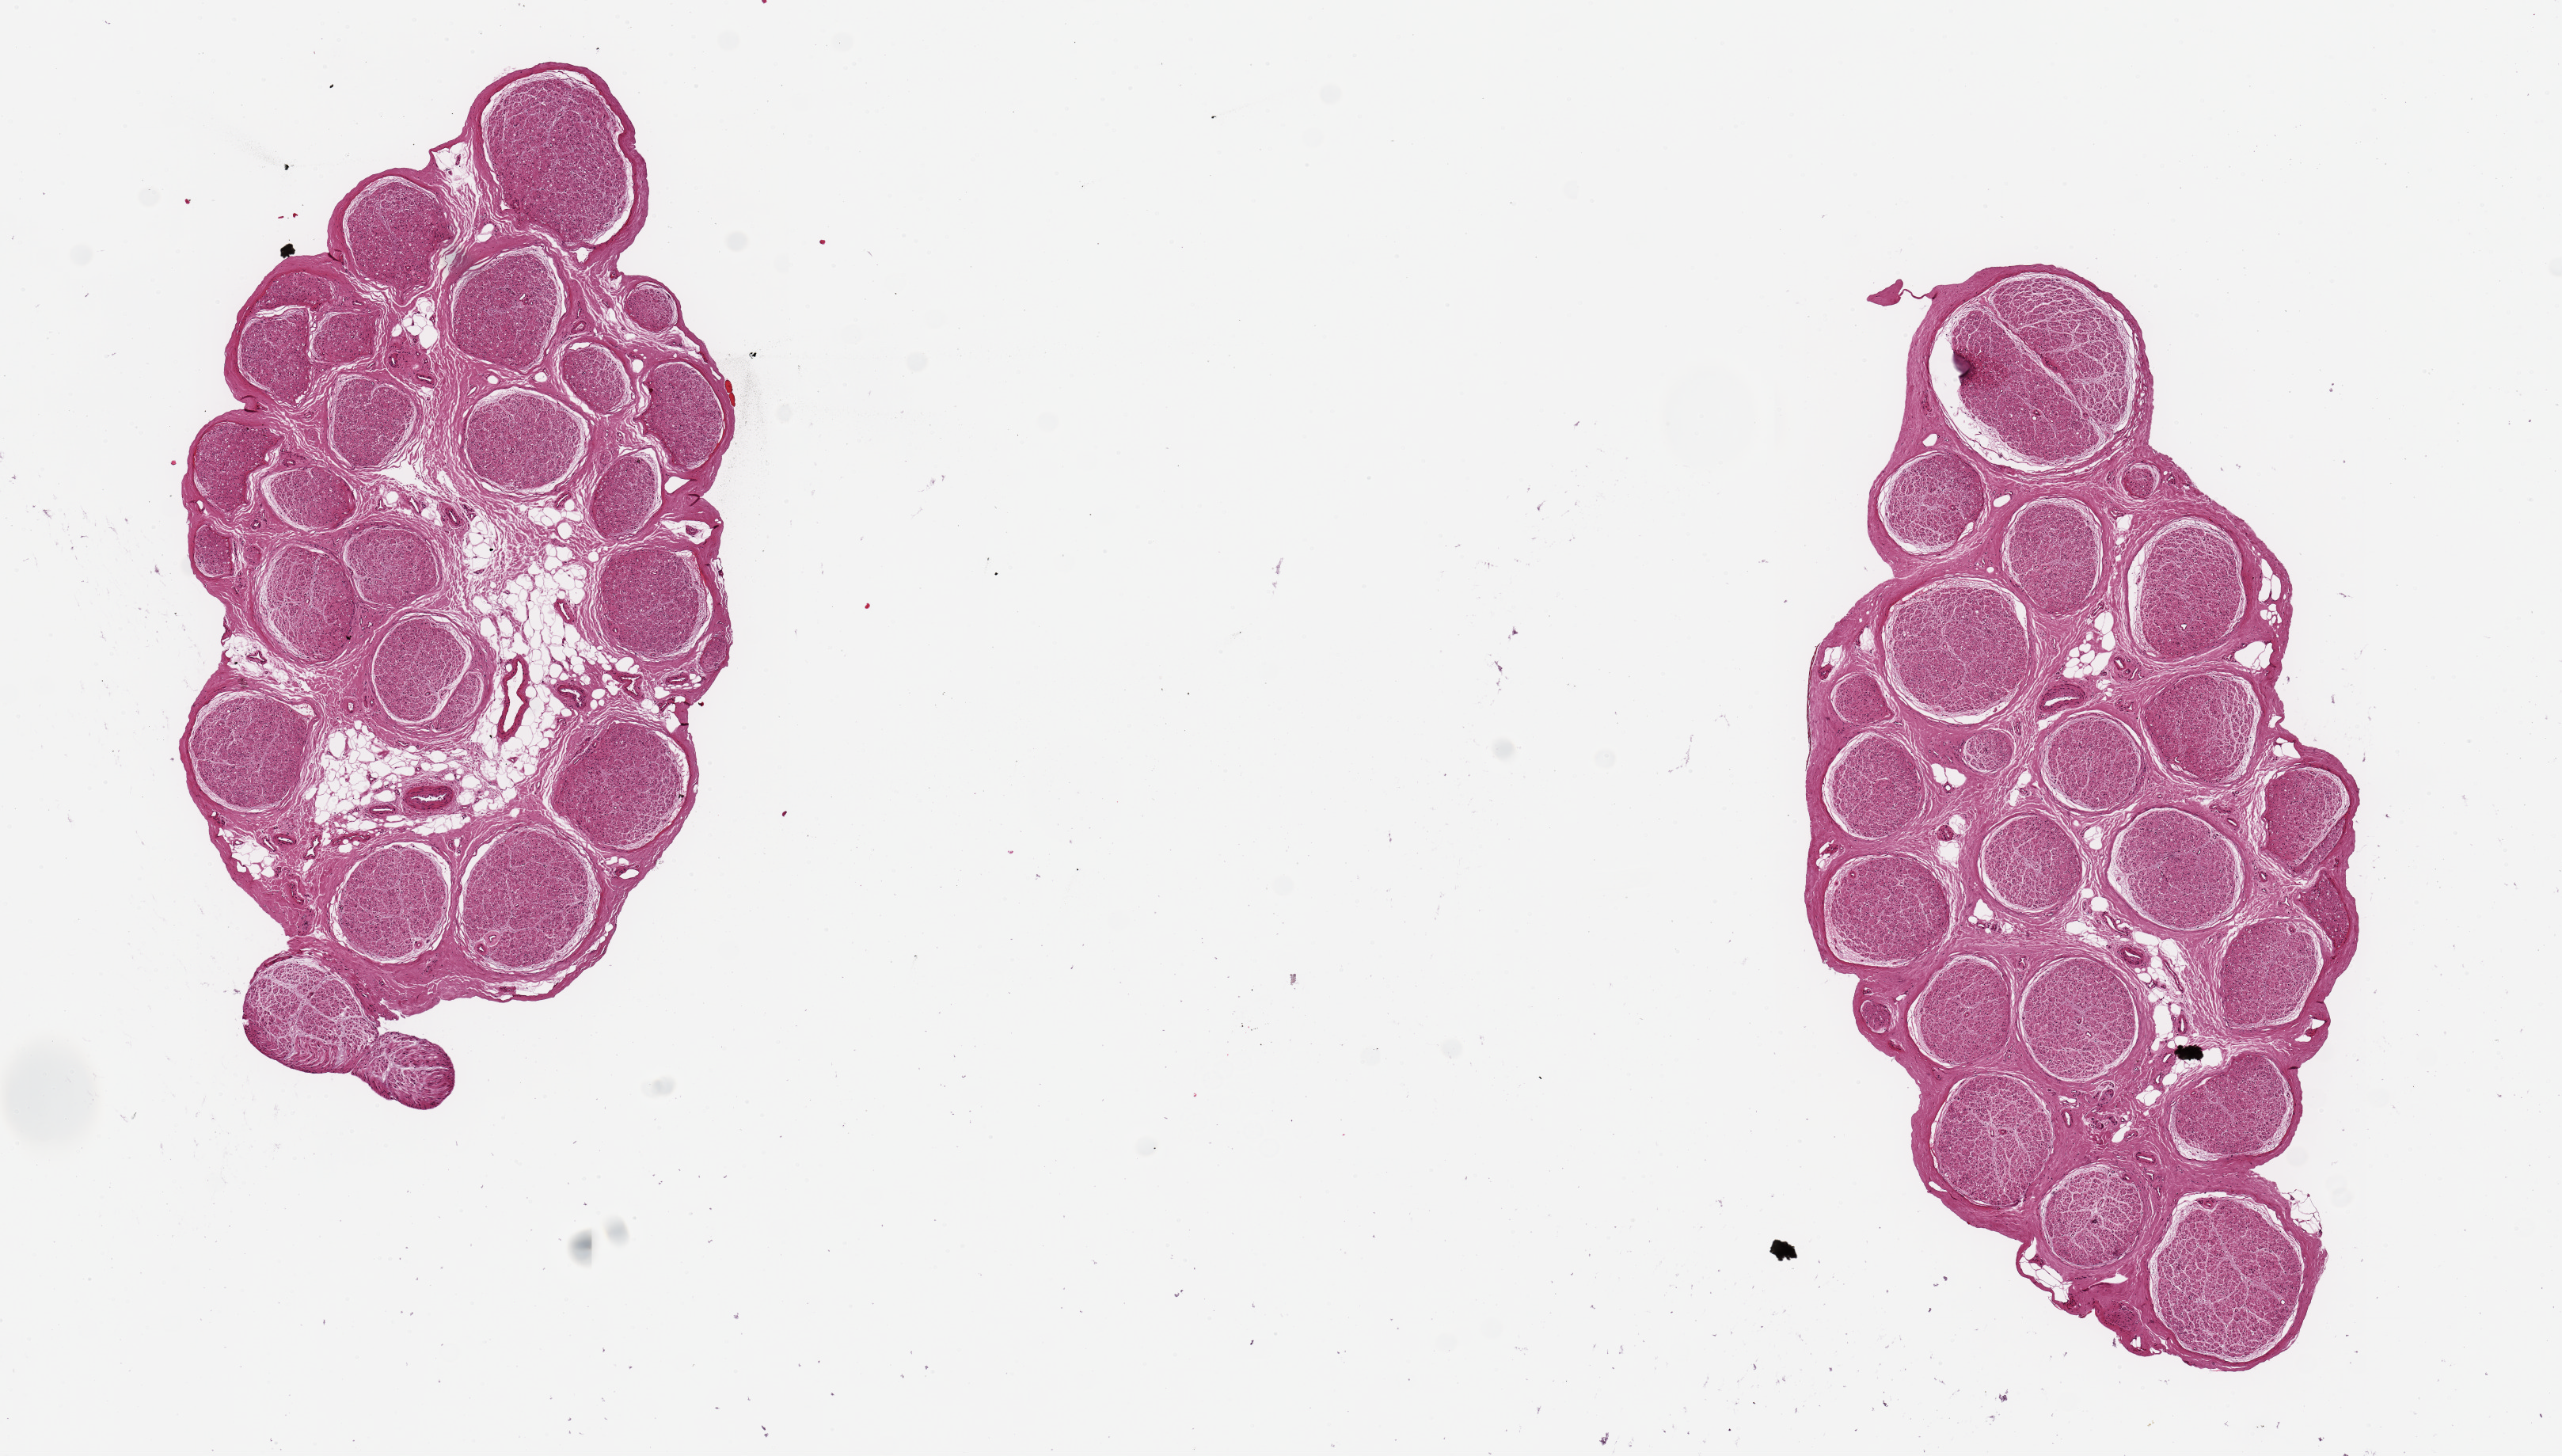
Digitized H&E-stained section, shown as a low-resolution overview of the whole scanned area (about 12.8 x 7.3 mm). PAXgene-fixed, paraffin-embedded tissue. Section of tibial nerve (target tissue). Donor tissue sample.
Pathologist's review note for this sample: 2 pieces ~5x3 mm; clean, no expernal adipose; ~10% internal adipose.